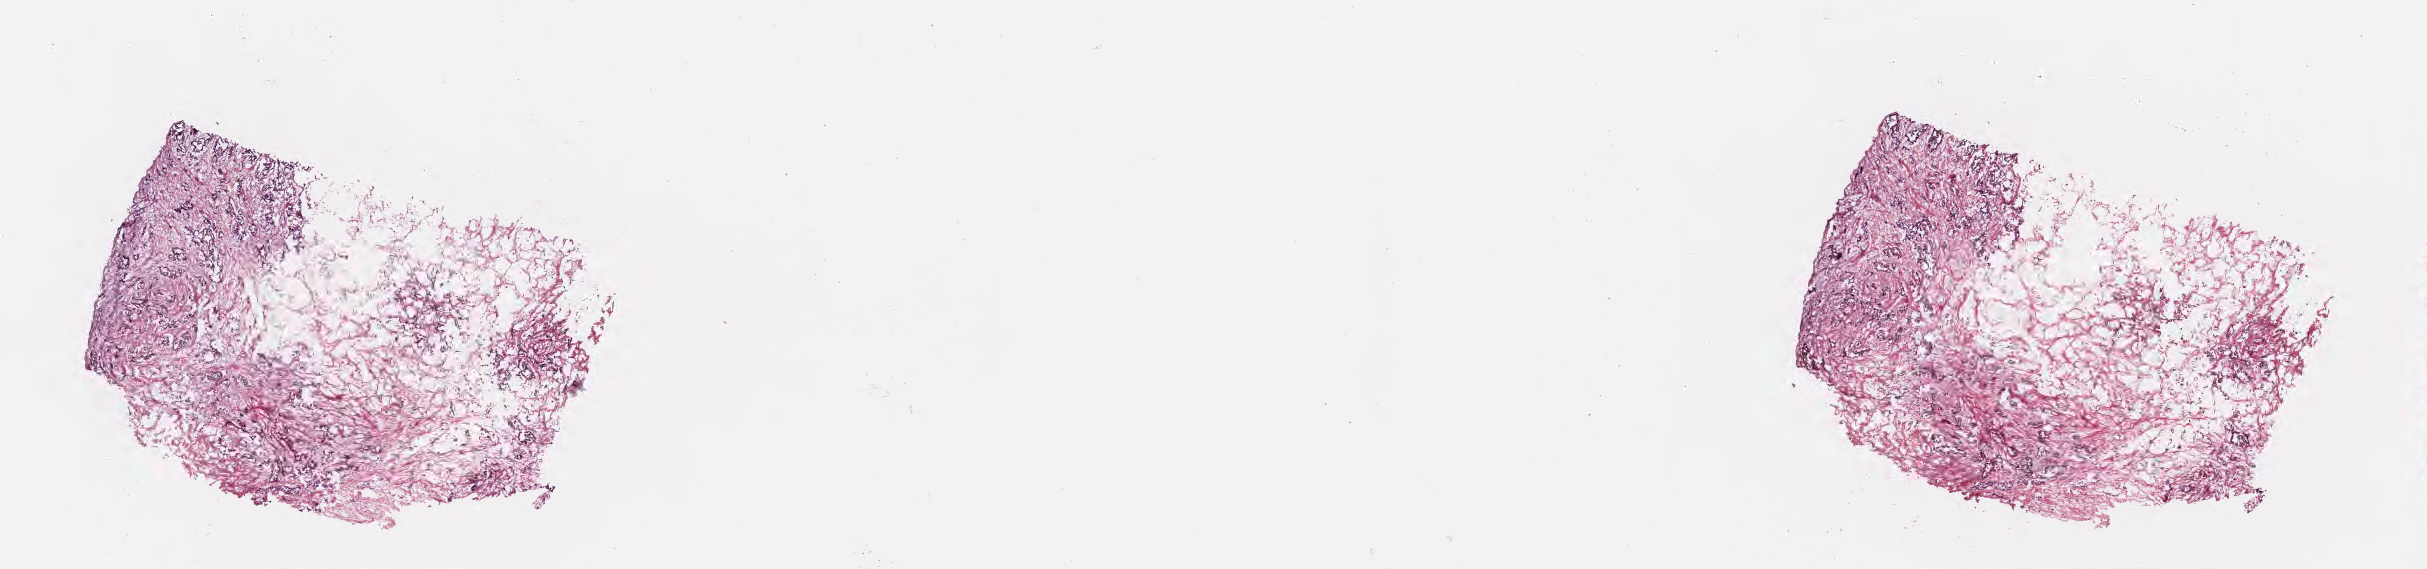
Digitized hematoxylin and eosin (H&E)-stained section — whole scanned area (about 19.6 x 4.6 mm) shown as a low-resolution overview, frozen section (tissue freezing medium), specimen: primary tumor, site: head of pancreas. Female patient; age at initial diagnosis 60 years. Tumor grade: G3 (poorly differentiated). Composition of this section per pathologist review: tumor cells 60%, tumor nuclei 60%, stromal cells 15%, necrosis 0%, normal cells 25%. Inflammatory infiltration, as recorded: lymphocyte infiltration 4%, monocyte infiltration 1%, neutrophil infiltration 5%.
Histologic diagnosis: Infiltrating duct carcinoma, NOS. AJCC pathologic stage: Stage III. Section: bottom of the tissue portion.